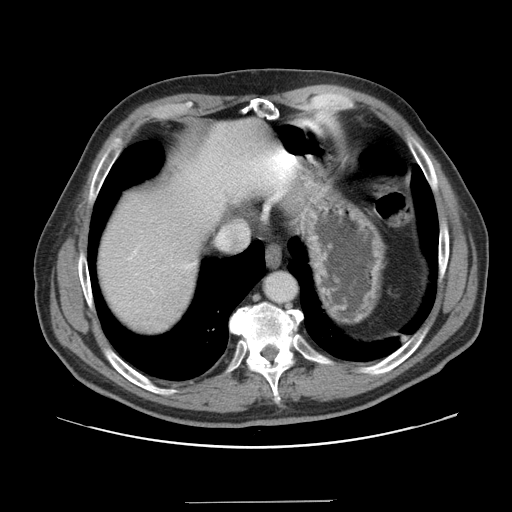
Contrast-enhanced abdominal CT, one axial slice; slice 137 of 151 in the series (ordered by position); 120 kVp; intravenous contrast given; soft-tissue window (W 400 / L 40 HU); 512 × 512 image matrix. Male patient, age 63 years. Case-level facts recorded for this patient, not image findings: diagnosis: colorectal cancer liver metastases, imaged before liver resection; multiple liver metastases: no; largest metastasis: 2.1 cm.
Annotated regions visible in this slice (manually delineated by an expert):
- hepatic veins: box from (x=220, y=235) to (x=224, y=239) px
- liver: (x=97, y=118)–(x=293, y=334)
- planned liver remnant (the part of the liver to remain after resection): (x=97, y=151)–(x=229, y=334)